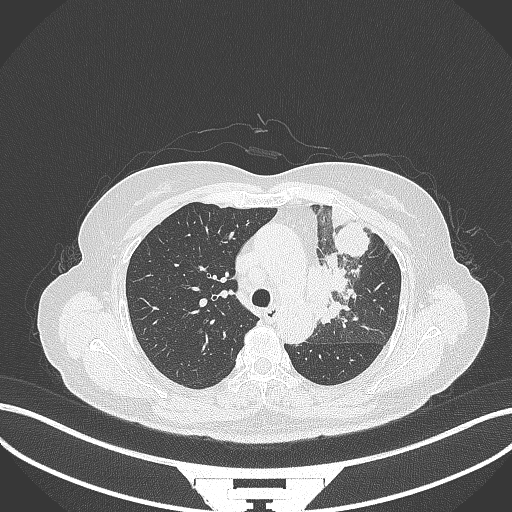
Chest CT, one axial slice. Slice 234 of 382 in the series (ordered by position). Reconstruction kernel B70f. 120 kVp. Lung window (W 1500 / L -600 HU). 1 mm slice thickness. 512 × 512 image matrix, field of view 400 × 400 mm. Patient: female, 64 years. Case-level facts recorded for this patient, not image findings: clinical TNM (as recorded): T2a N2 M0.
Outlined on this slice (bounding box drawn by a radiologist):
- lung tumour (recorded histology: adenocarcinoma): box from (x=308, y=249) to (x=358, y=326) px
- lung tumour (recorded histology: adenocarcinoma): (x=334, y=217)–(x=372, y=258)